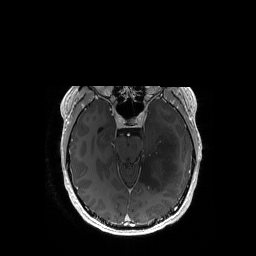
Brain MRI from a brain-tumour surgery series, one axial slice; slice 110 of 192 in the series (ordered by position); T1-weighted post-contrast; 1 mm slice thickness; 256 × 256 image matrix. From the clinical record (not read from this slice): histopathology: Astrocytoma; WHO grade: 3; IDH mutation: yes.
Annotated regions visible in this slice (manually delineated by an expert):
- tumour: box from (x=139, y=130) to (x=178, y=191) px